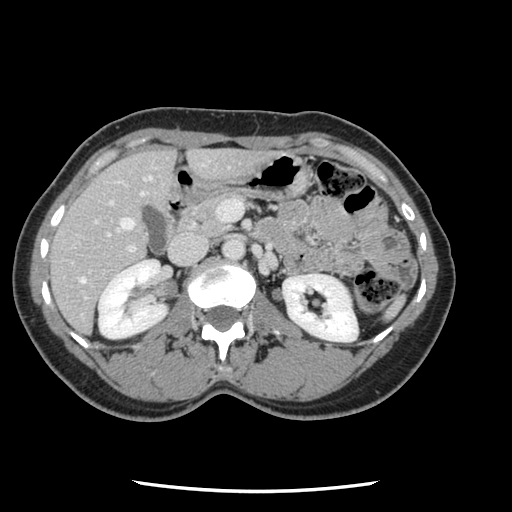
Contrast-enhanced abdominal CT, one axial slice; slice 51 of 134 in the series (ordered by position); intravenous contrast given; soft-tissue window (W 400 / L 40 HU); 2.5 mm slice thickness; 512 × 512 image matrix. Female patient, age 43 years. Case-level facts recorded for this patient, not image findings: diagnosis: colorectal cancer liver metastases, imaged before liver resection; multiple liver metastases: yes; largest metastasis: 3.4 cm; chemotherapy before resection: no.
Structures marked on this image (expert manual segmentation):
- hepatic veins: bounding box [x1, y1, x2, y2] px = [79, 176, 153, 284]
- liver: [51, 149, 262, 333]
- planned liver remnant (the part of the liver to remain after resection): [51, 149, 175, 331]
- portal vein (with intrahepatic branches): [71, 201, 243, 300]